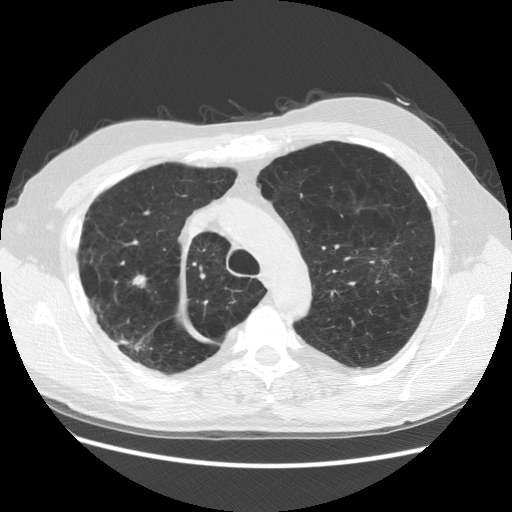
Low-dose screening chest CT, one axial slice; position 102 of 137 along the scan axis; reconstruction kernel STANDARD; lung window (W 1500 / L -600 HU); 2.5 mm slice thickness; 512 × 512 image matrix, field of view 377 × 377 mm.
Annotated regions visible in this slice (expert manual segmentation):
- lesion 1 (tumor, upper lobe of right lung): bounding box <132,275,147,288> (left, top, right, bottom; pixels)
- lesion 2 (nodule, upper lobe of right lung): <118,336,148,353>